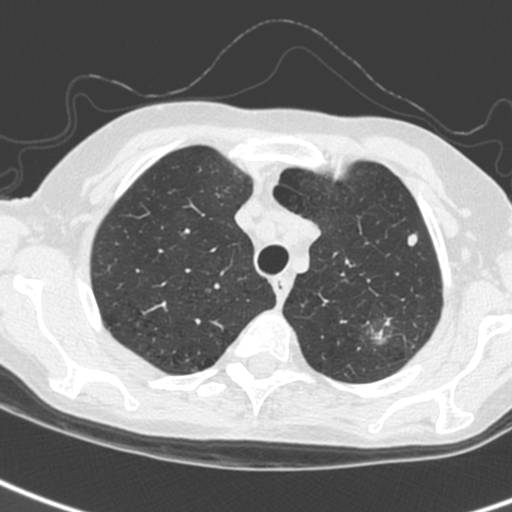
Low-dose screening chest CT, one axial slice; 120 kVp; lung window (W 1500 / L -600 HU); 1.3 mm slice thickness; 512 × 512 image matrix, field of view 284 × 284 mm.
Annotated regions visible in this slice (expert manual segmentation):
- lesion 2 (tumor, upper lobe of left lung): box from (x=408, y=234) to (x=418, y=246) px